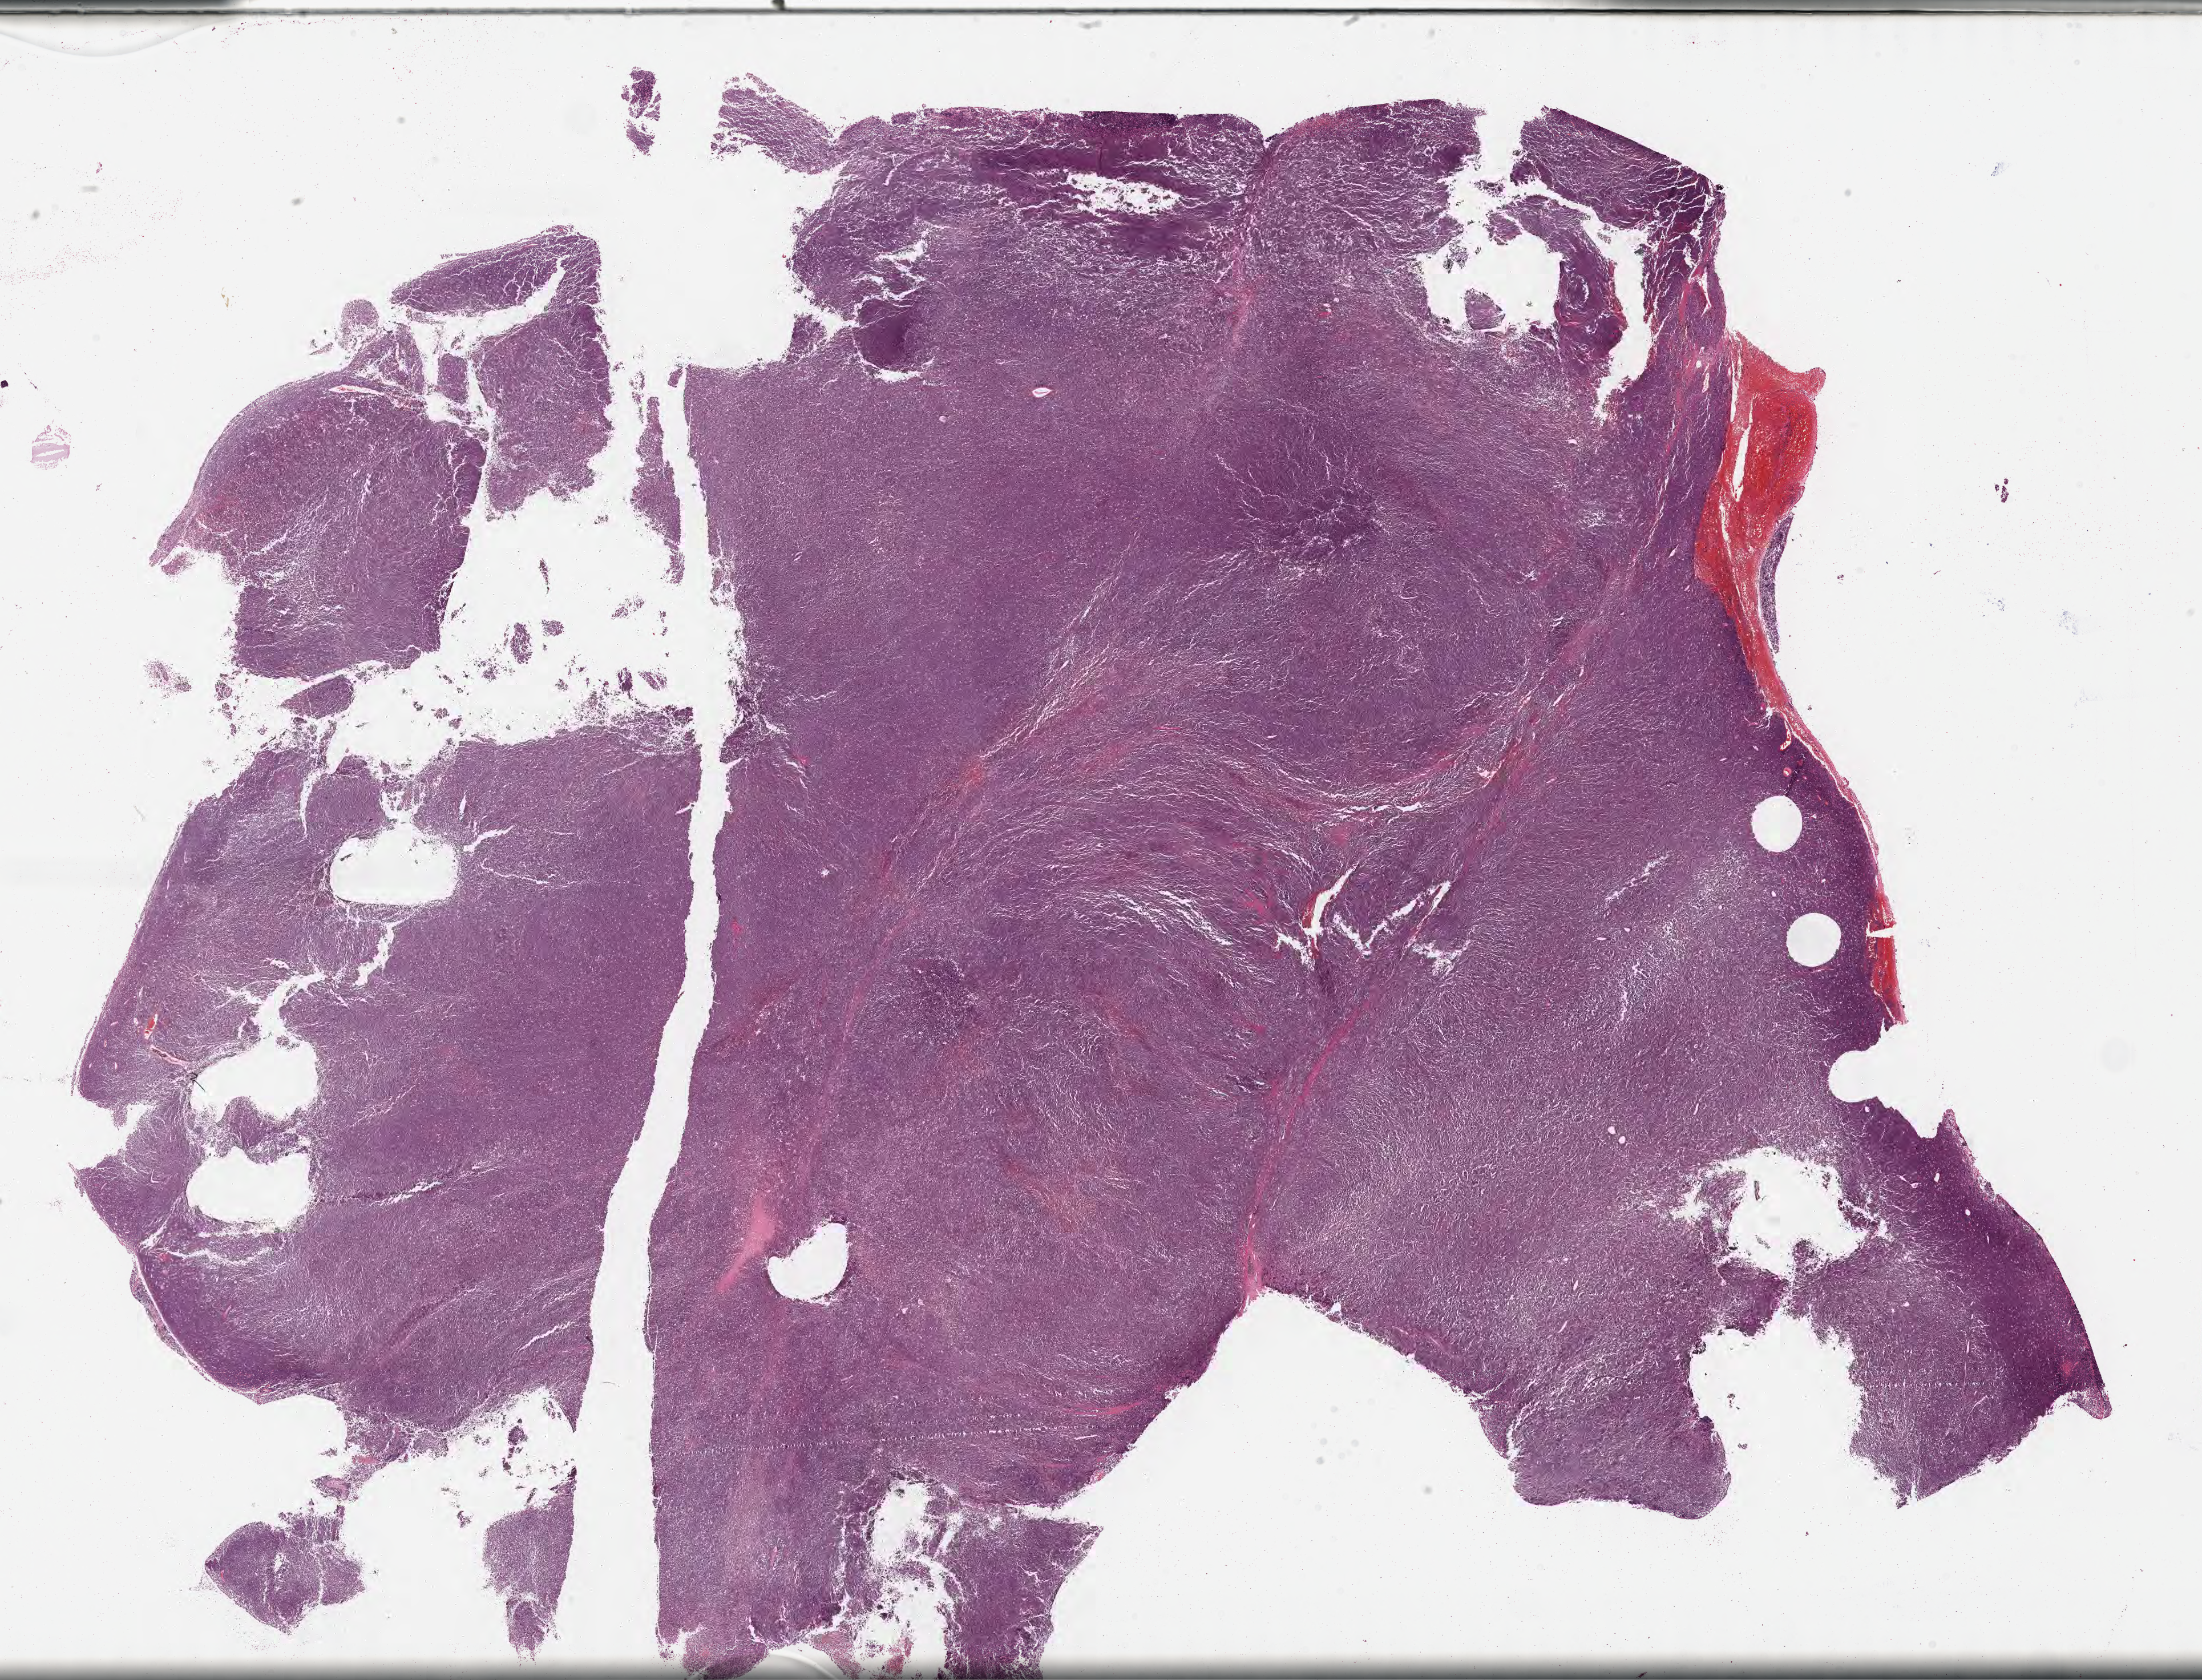
H&E whole-slide image, whole scanned area (about 31.2 x 23.8 mm) shown as a low-resolution overview. Formalin-fixed paraffin-embedded section. Primary tumor. Male patient, 15 years old. Composition of this section per pathologist review: tumor cells 90%, tumor nuclei 95%.
Diagnosis: Burkitt lymphoma, NOS.